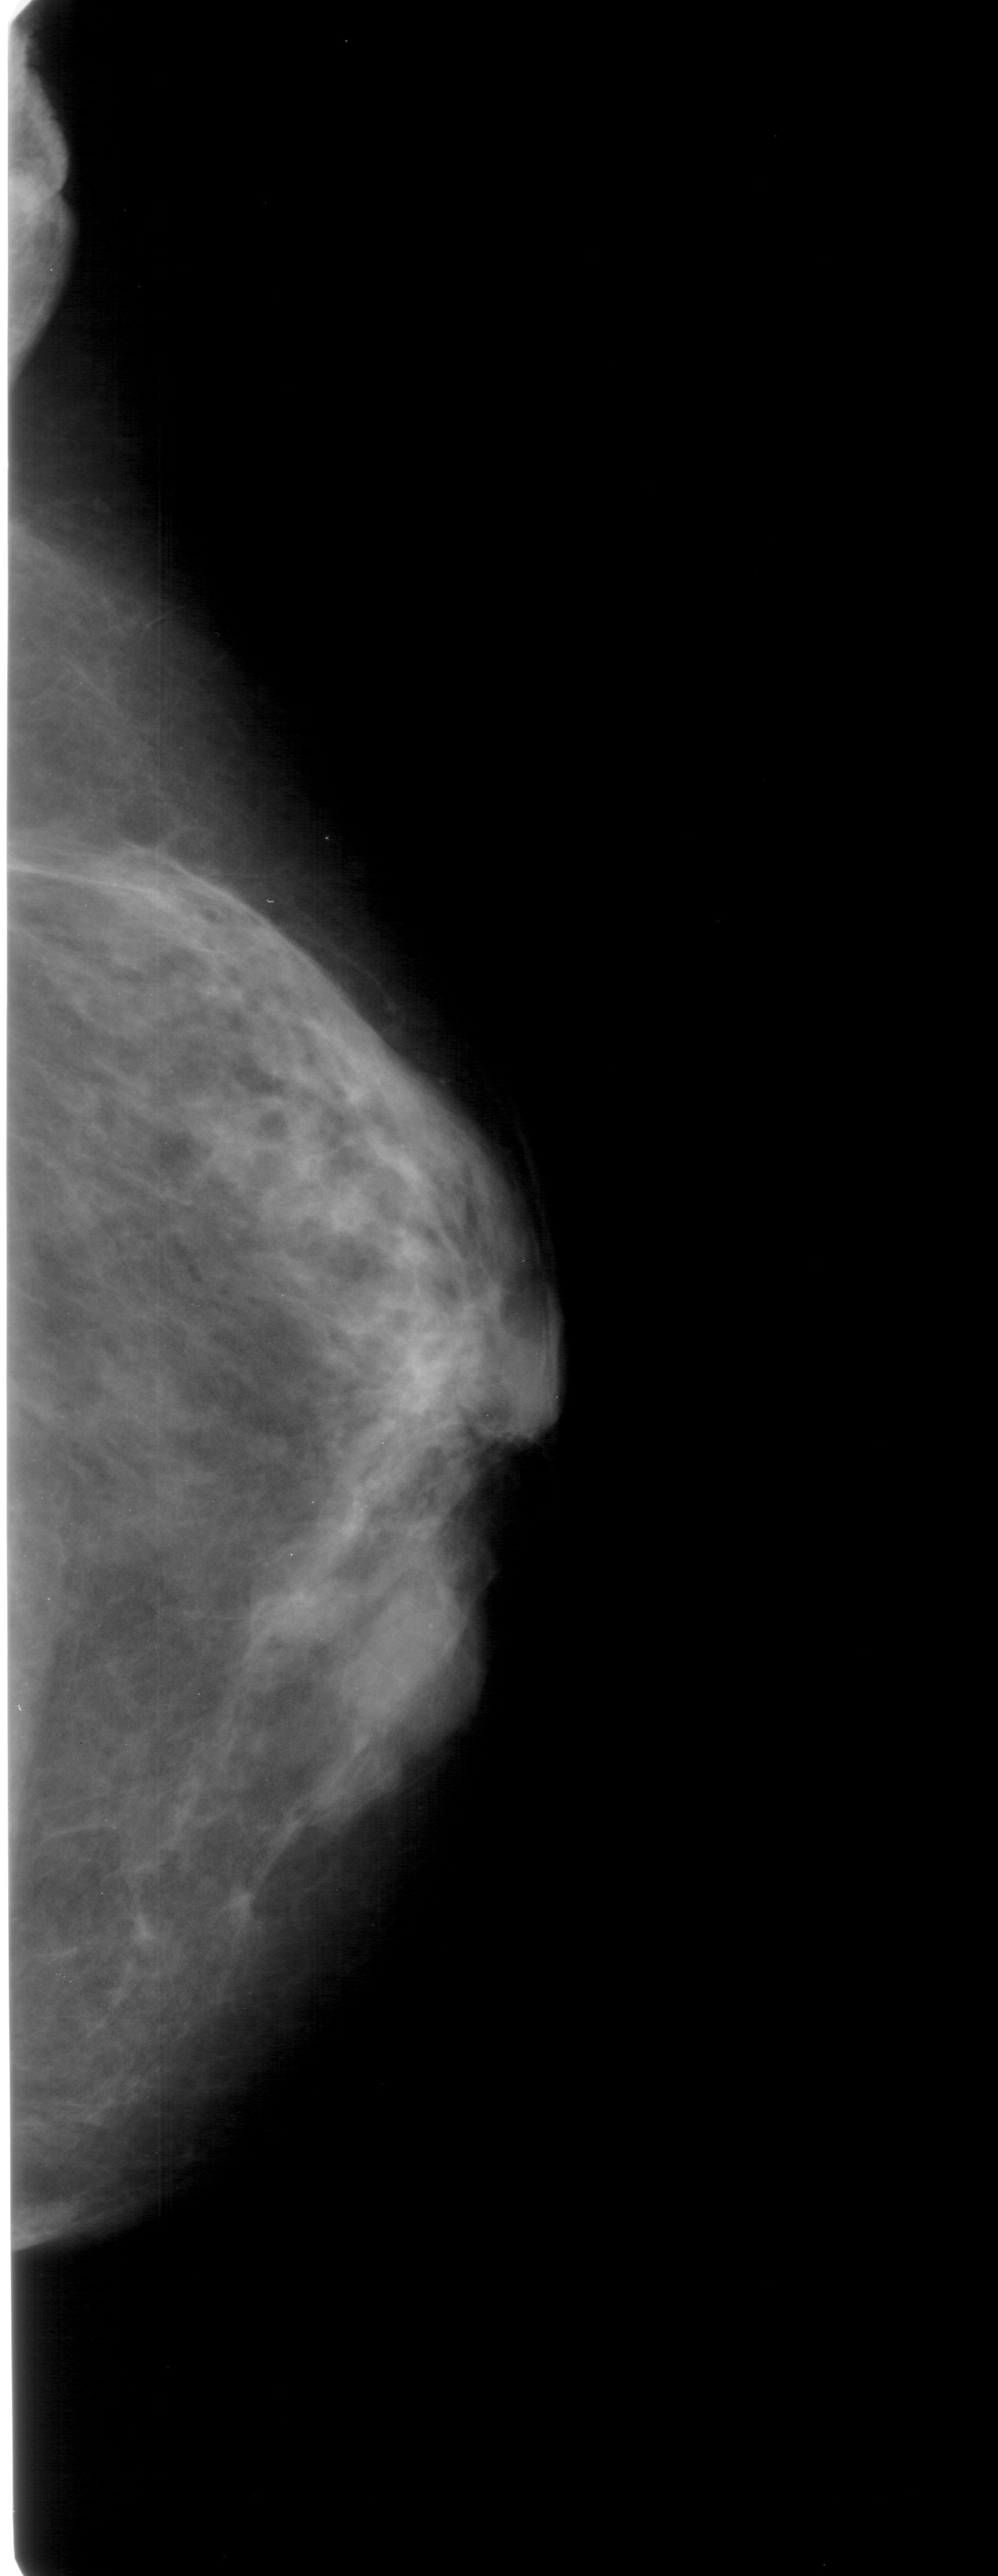
Mammogram (digitized film); right breast; craniocaudal (CC) view; 998 × 2576 image matrix.
Marked abnormalities (boxes around the expert regions of interest):
- calcifications, morphology pleomorphic, distribution clustered; BI-RADS assessment category 4; subtlety rating 2 on a 1 (subtle) to 5 (obvious) scale; pathology (as recorded): malignant: bounding box <315,1466,412,1567> (left, top, right, bottom; pixels)